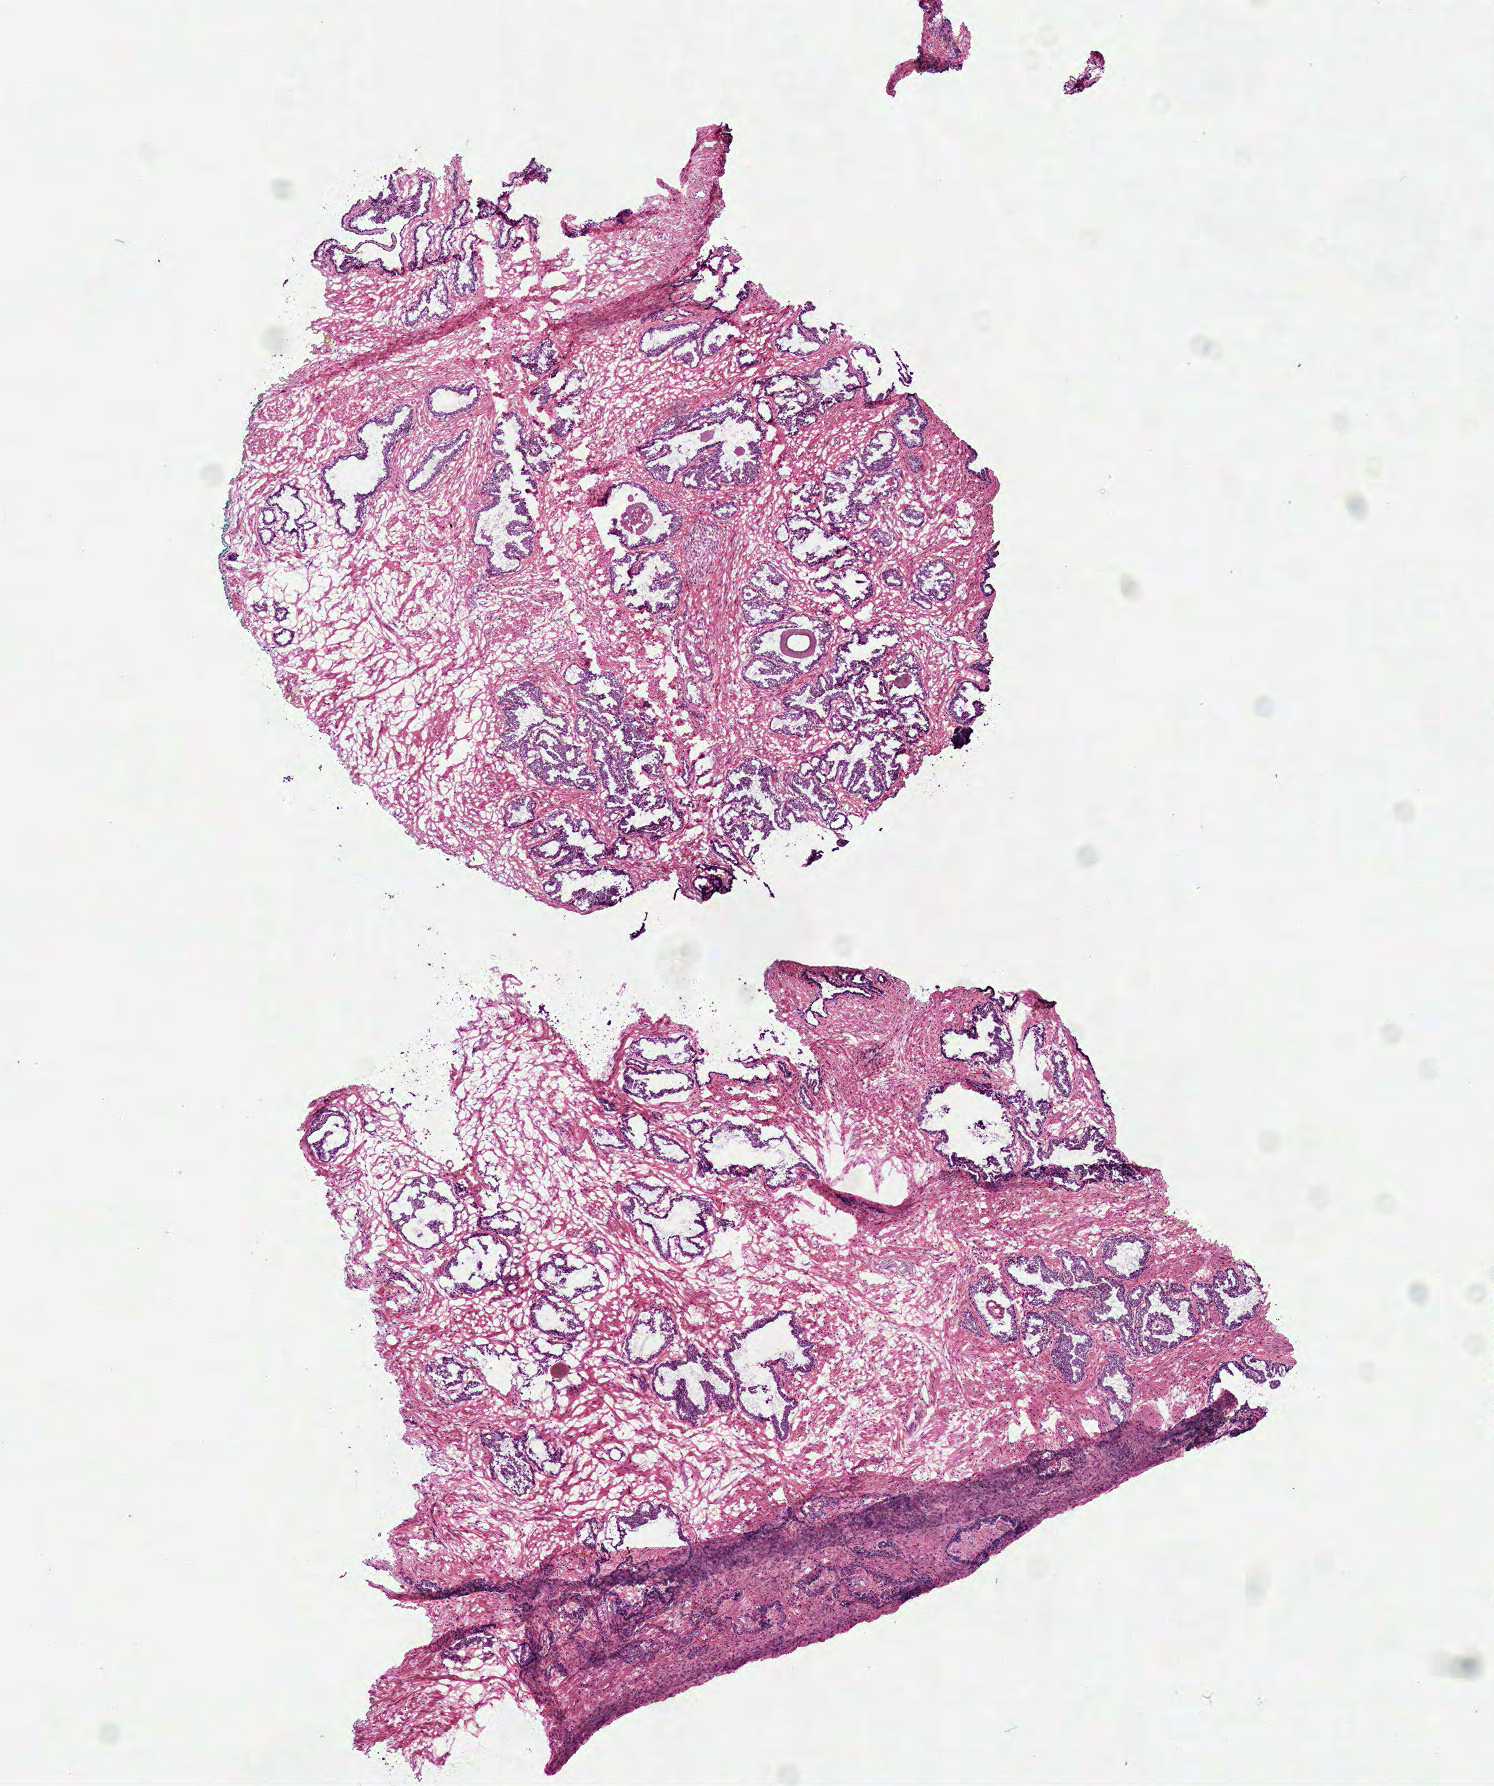
Digitized H&E tissue section (whole slide) — shown as a low-resolution overview of the whole scanned area (about 5.9 x 7.0 mm), frozen section from the top of the tissue portion, prostate, solid tissue normal (non-tumour tissue) sample. Patient: male, age at initial diagnosis 51 years.
This section: solid tissue normal (non-tumour) sample from the same patient. Patient diagnosis: Acinar cell carcinoma (prostate gland).